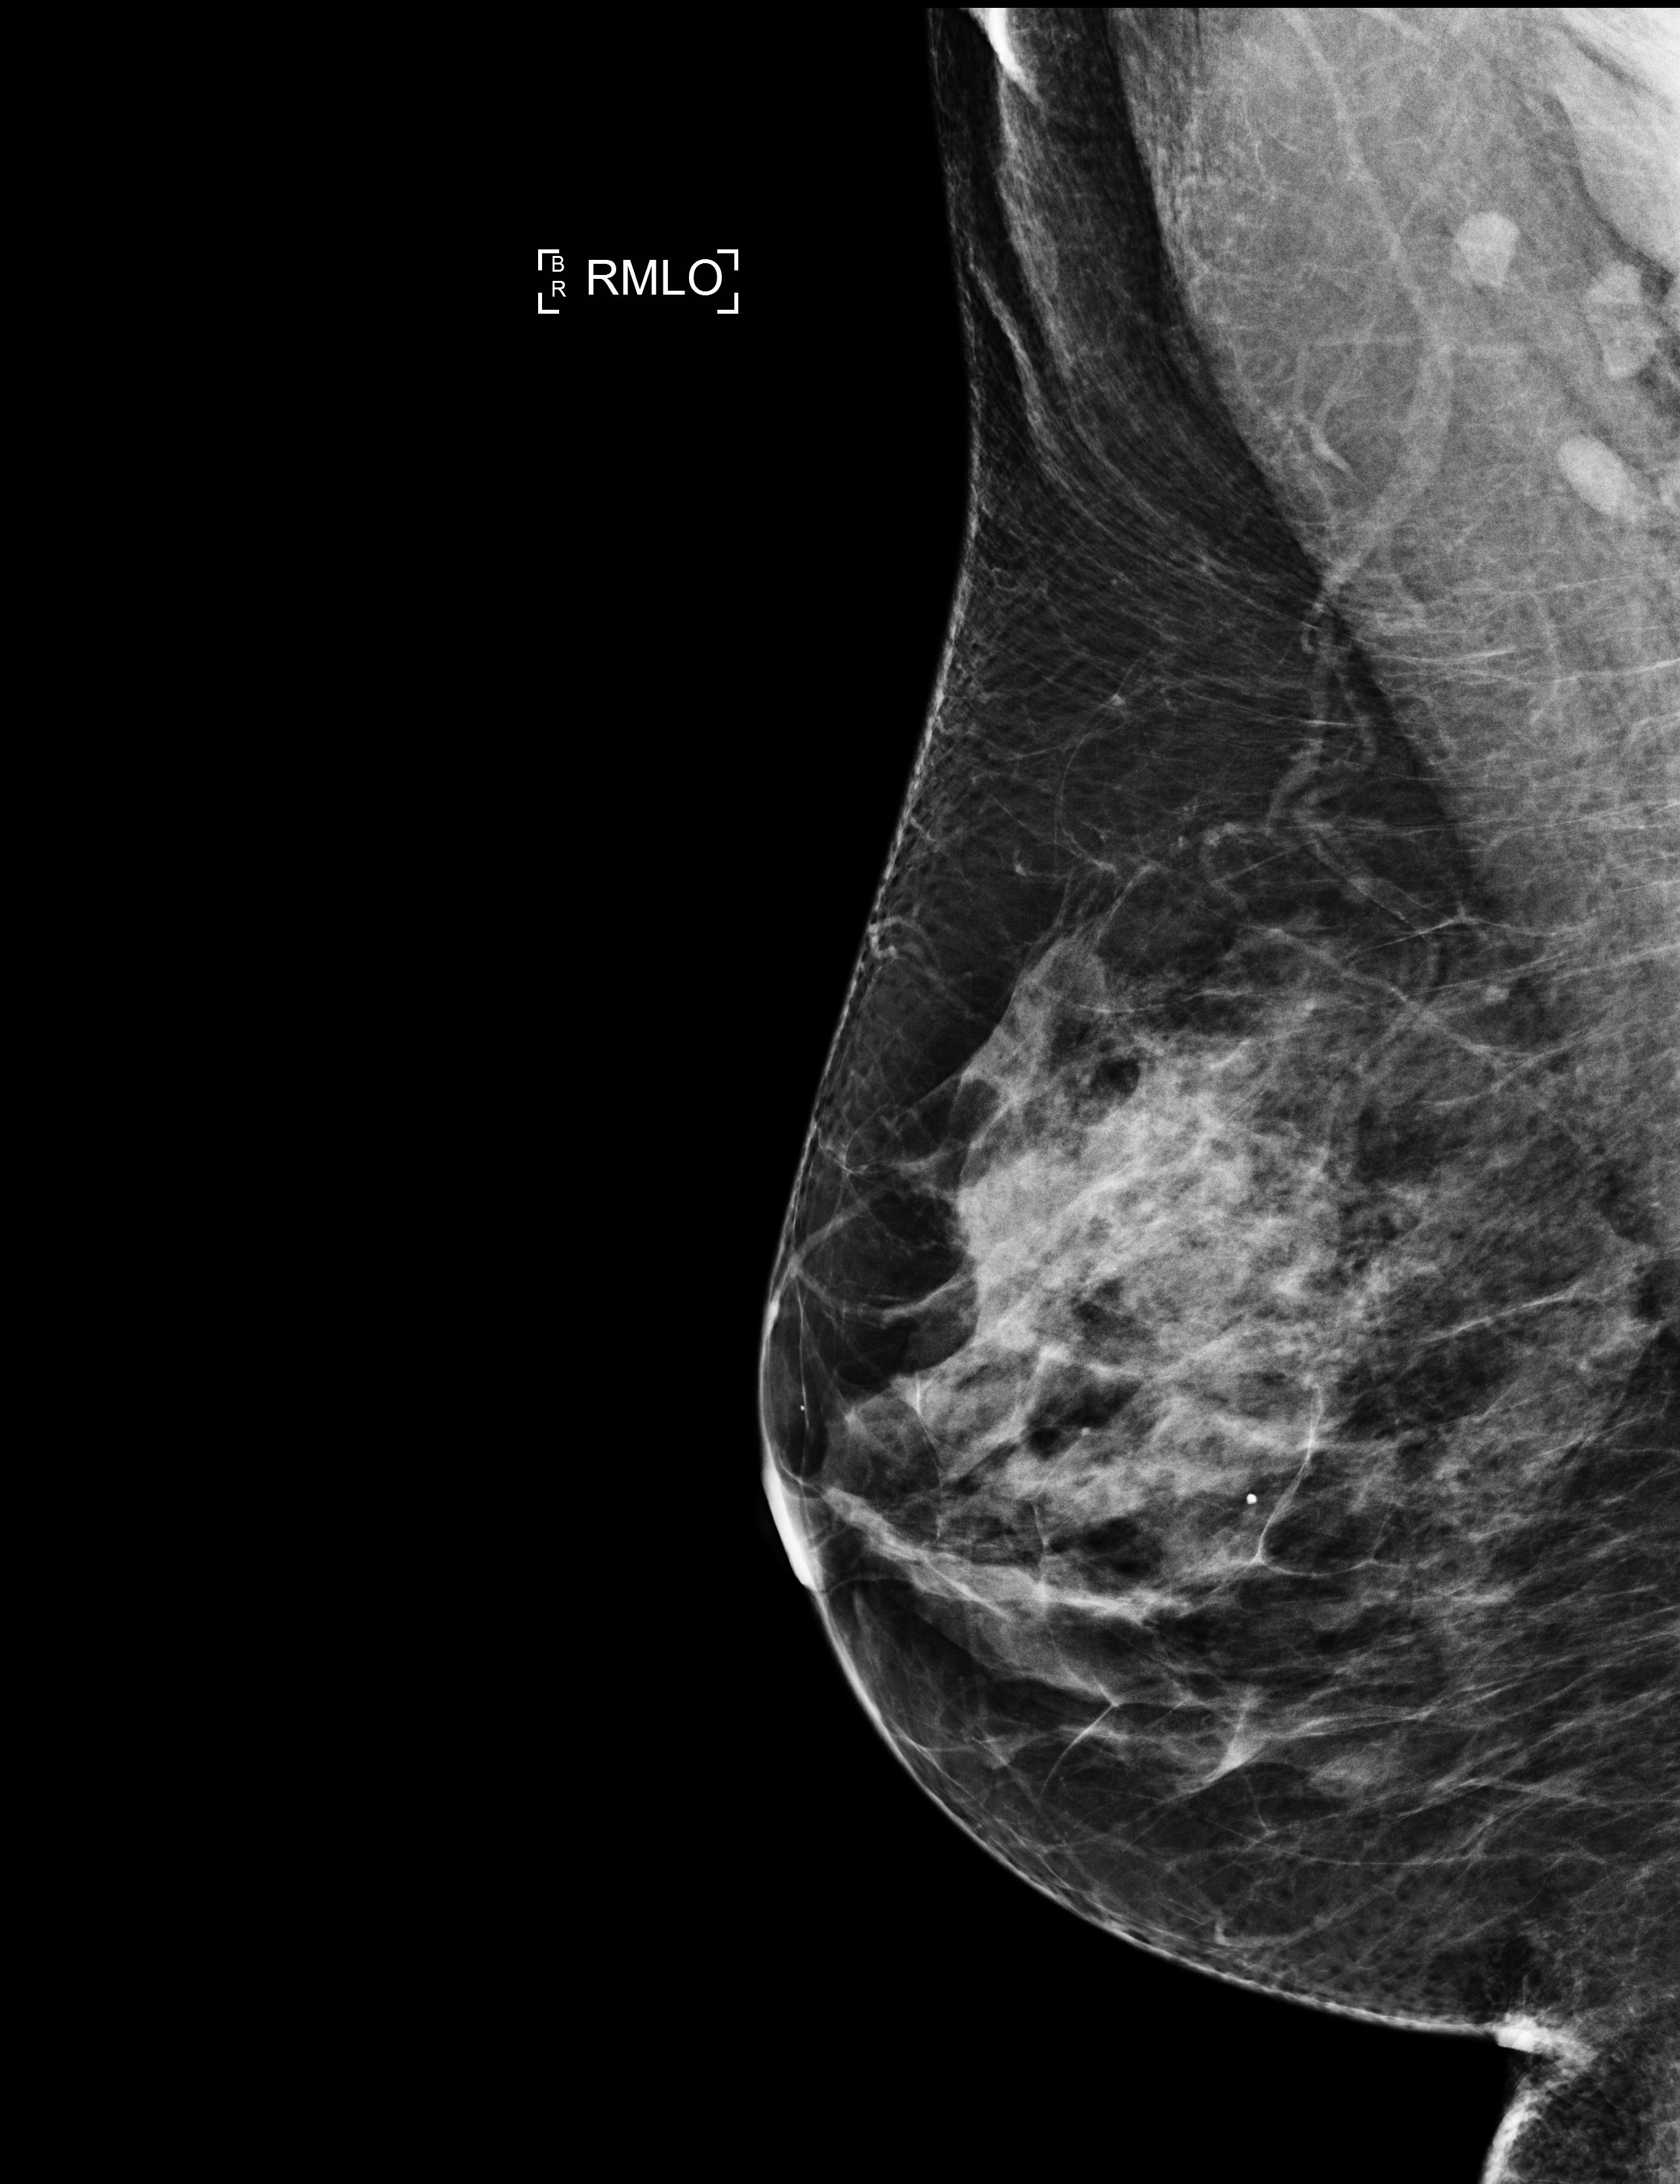
Annual screening mammography examination, system: Selenia Dimensions. Patient: female, 67 years.
Image type: full-field digital mammogram. Breast: right. Projection: MLO view.